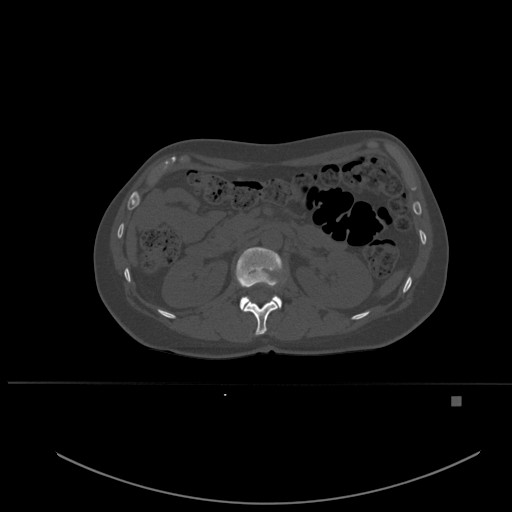
CT including the spine, one axial slice; position 244 of 651 along the scan axis; bone window (W 1800 / L 400 HU); 1.5 mm slice thickness; 512 × 512 image matrix. Female patient, age 49 years. From the clinical record (not read from this slice): primary cancer: breast; vertebrae with lytic lesions (as recorded): L3, T12, L4.
Structures marked on this image (semi-automatically segmented with operator editing):
- L1 vertebra: bounding box (x1, y1, x2, y2) in pixels: (235, 247, 283, 310)
- T12 vertebra: (243, 300, 278, 335)